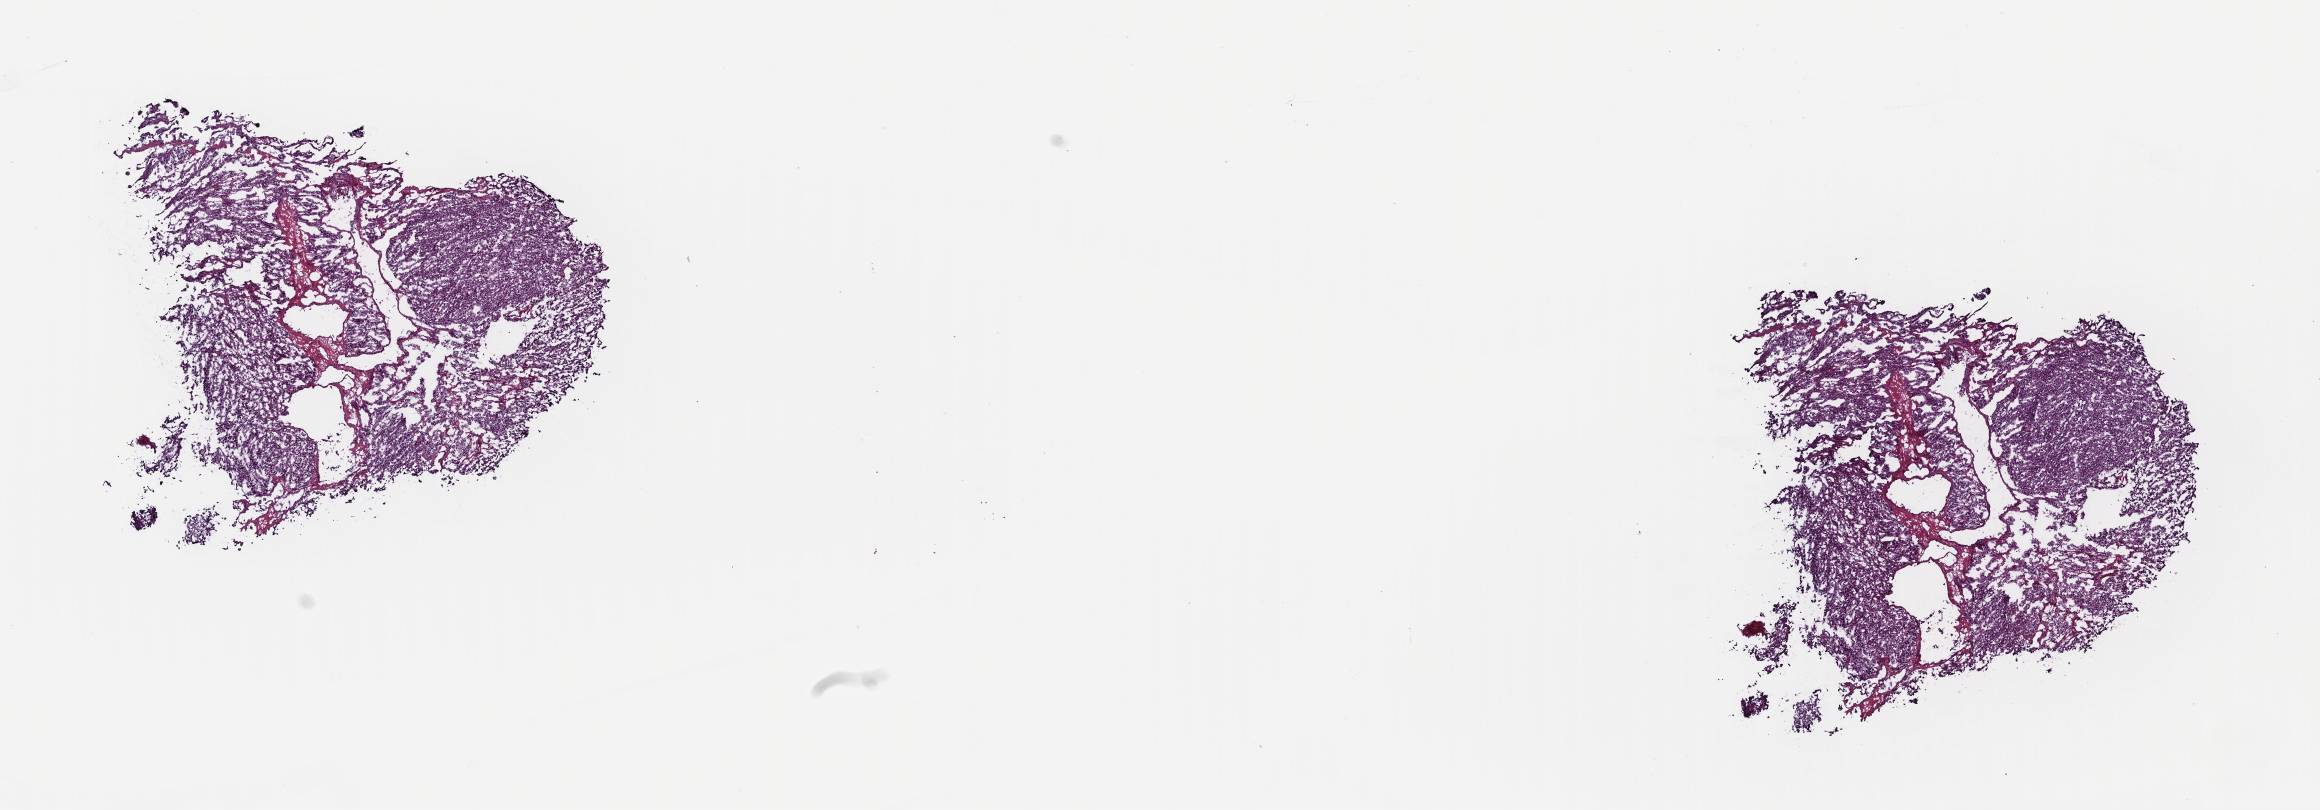
H&E-stained whole-slide image, shown as a low-resolution overview of the whole scanned area (about 18.2 x 6.4 mm, slide scanned at 40x), frozen section, adrenal cortex, primary tumour sample. Patient: male, age at initial diagnosis 37 years. Composition of this section per pathologist review: tumour cells 90%, tumour nuclei 90%, normal cells 0%, stromal cells 1%, necrosis 9%. Infiltration values recorded for this section: lymphocyte infiltration 0%, monocyte infiltration 0%, neutrophil infiltration 0%.
• histologic diagnosis: Adrenal cortical carcinoma (cortex of adrenal gland)
• laterality: left